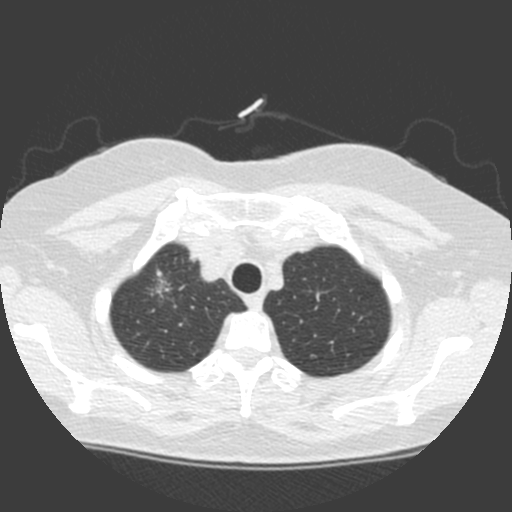
Low-dose screening chest CT, one axial slice. Slice 138 of 155 in the series (ordered by position). Lung window (W 1500 / L -600 HU). 2 mm slice thickness. 512 × 512 image matrix, field of view 314 × 314 mm.
Structures marked on this image (expert manual segmentation):
- lesion 1 (tumor, upper lobe of right lung): box from (x=151, y=270) to (x=172, y=298) px